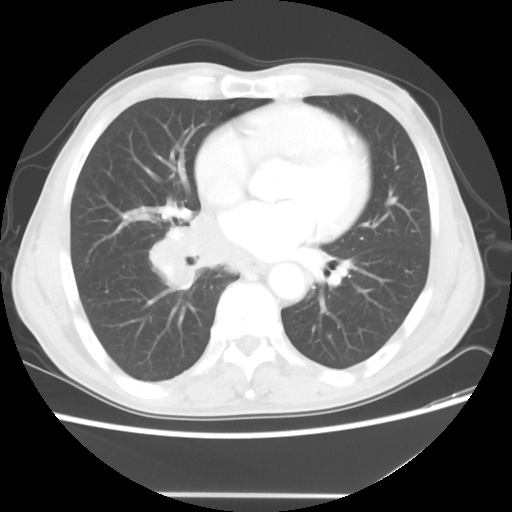
Chest CT, one axial slice. Slice 23 of 56 in the series (ordered by position). Reconstruction kernel STANDARD. Lung window (W 1500 / L -600 HU). 512 × 512 image matrix, field of view 344 × 344 mm. Male patient, age 65 years. From the clinical record (not read from this slice): clinical TNM (as recorded): T1c N3 M0.
Outlined on this slice (bounding box drawn by a radiologist):
- lung tumour (recorded histology: small cell carcinoma): bounding box <148,201,266,289> (left, top, right, bottom; pixels)